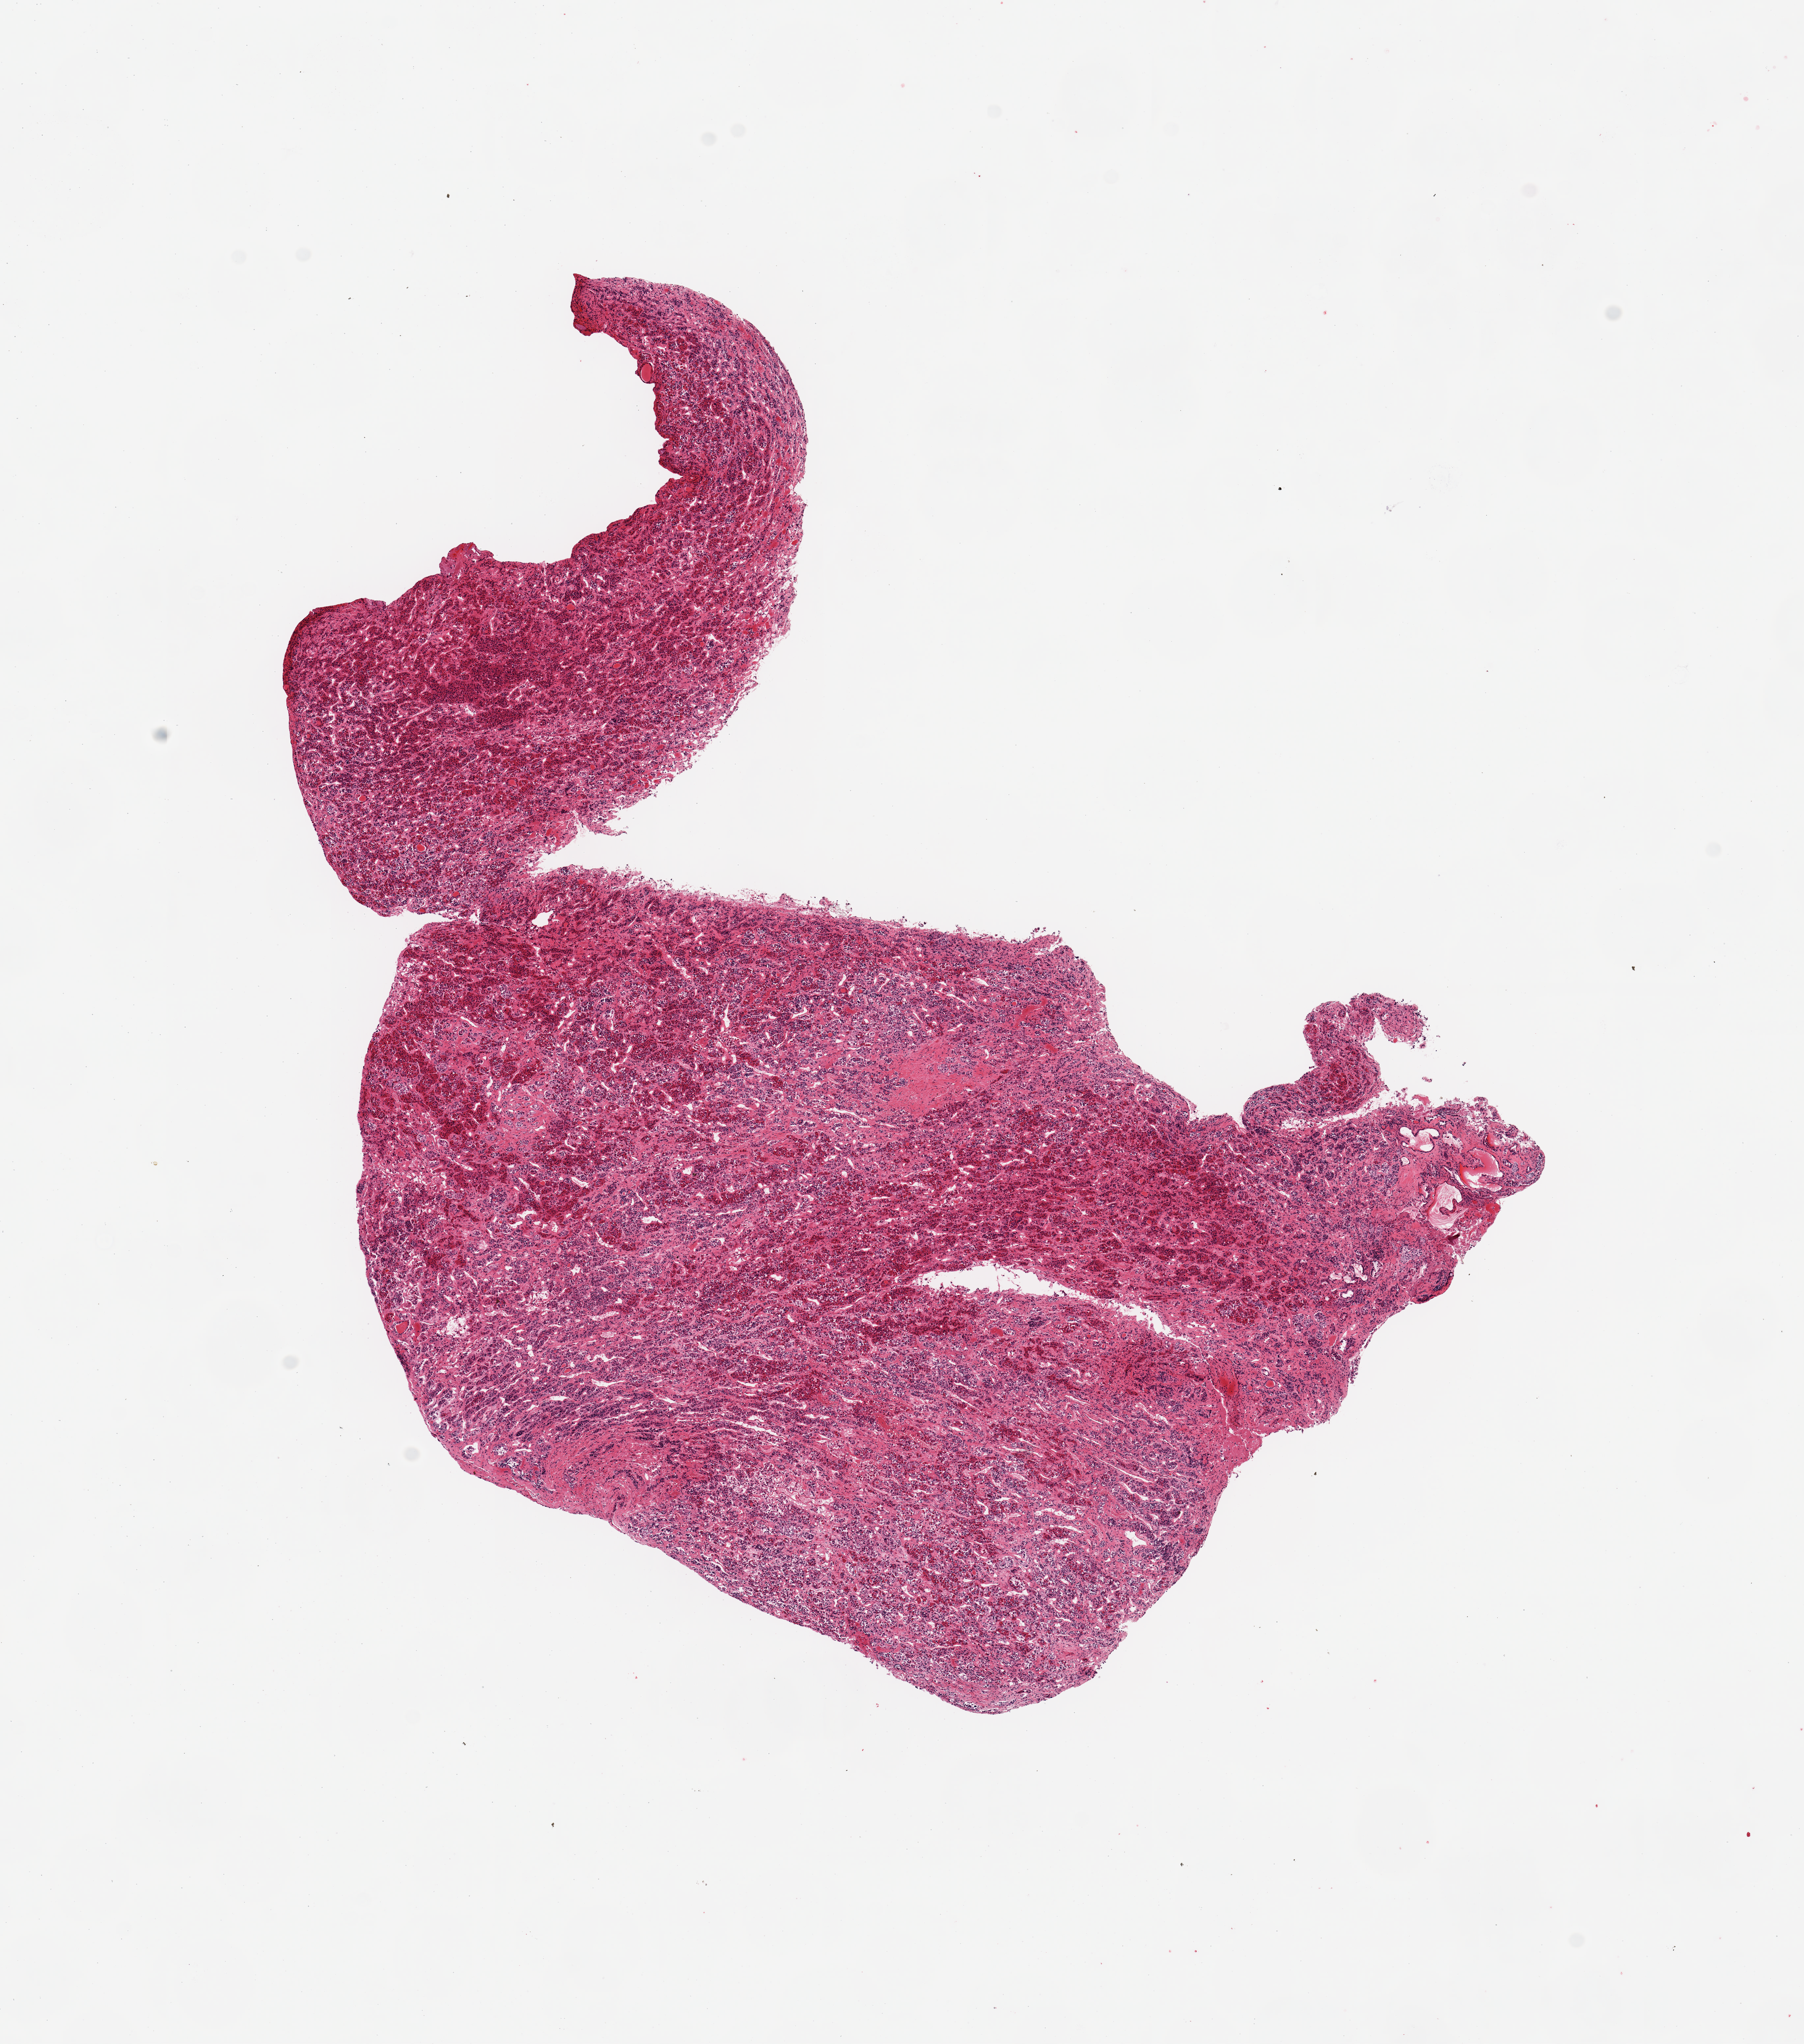
Hematoxylin and eosin (H&E) whole-slide image, whole scanned area (about 10.8 x 12.3 mm) shown as a low-resolution overview. PAXgene-fixed, paraffin-embedded tissue. Section of pituitary (target tissue). Donor tissue sample.
• pathologist's review note for this sample: 1 piece; all anterior lobe, no neurohypophysis in this cut